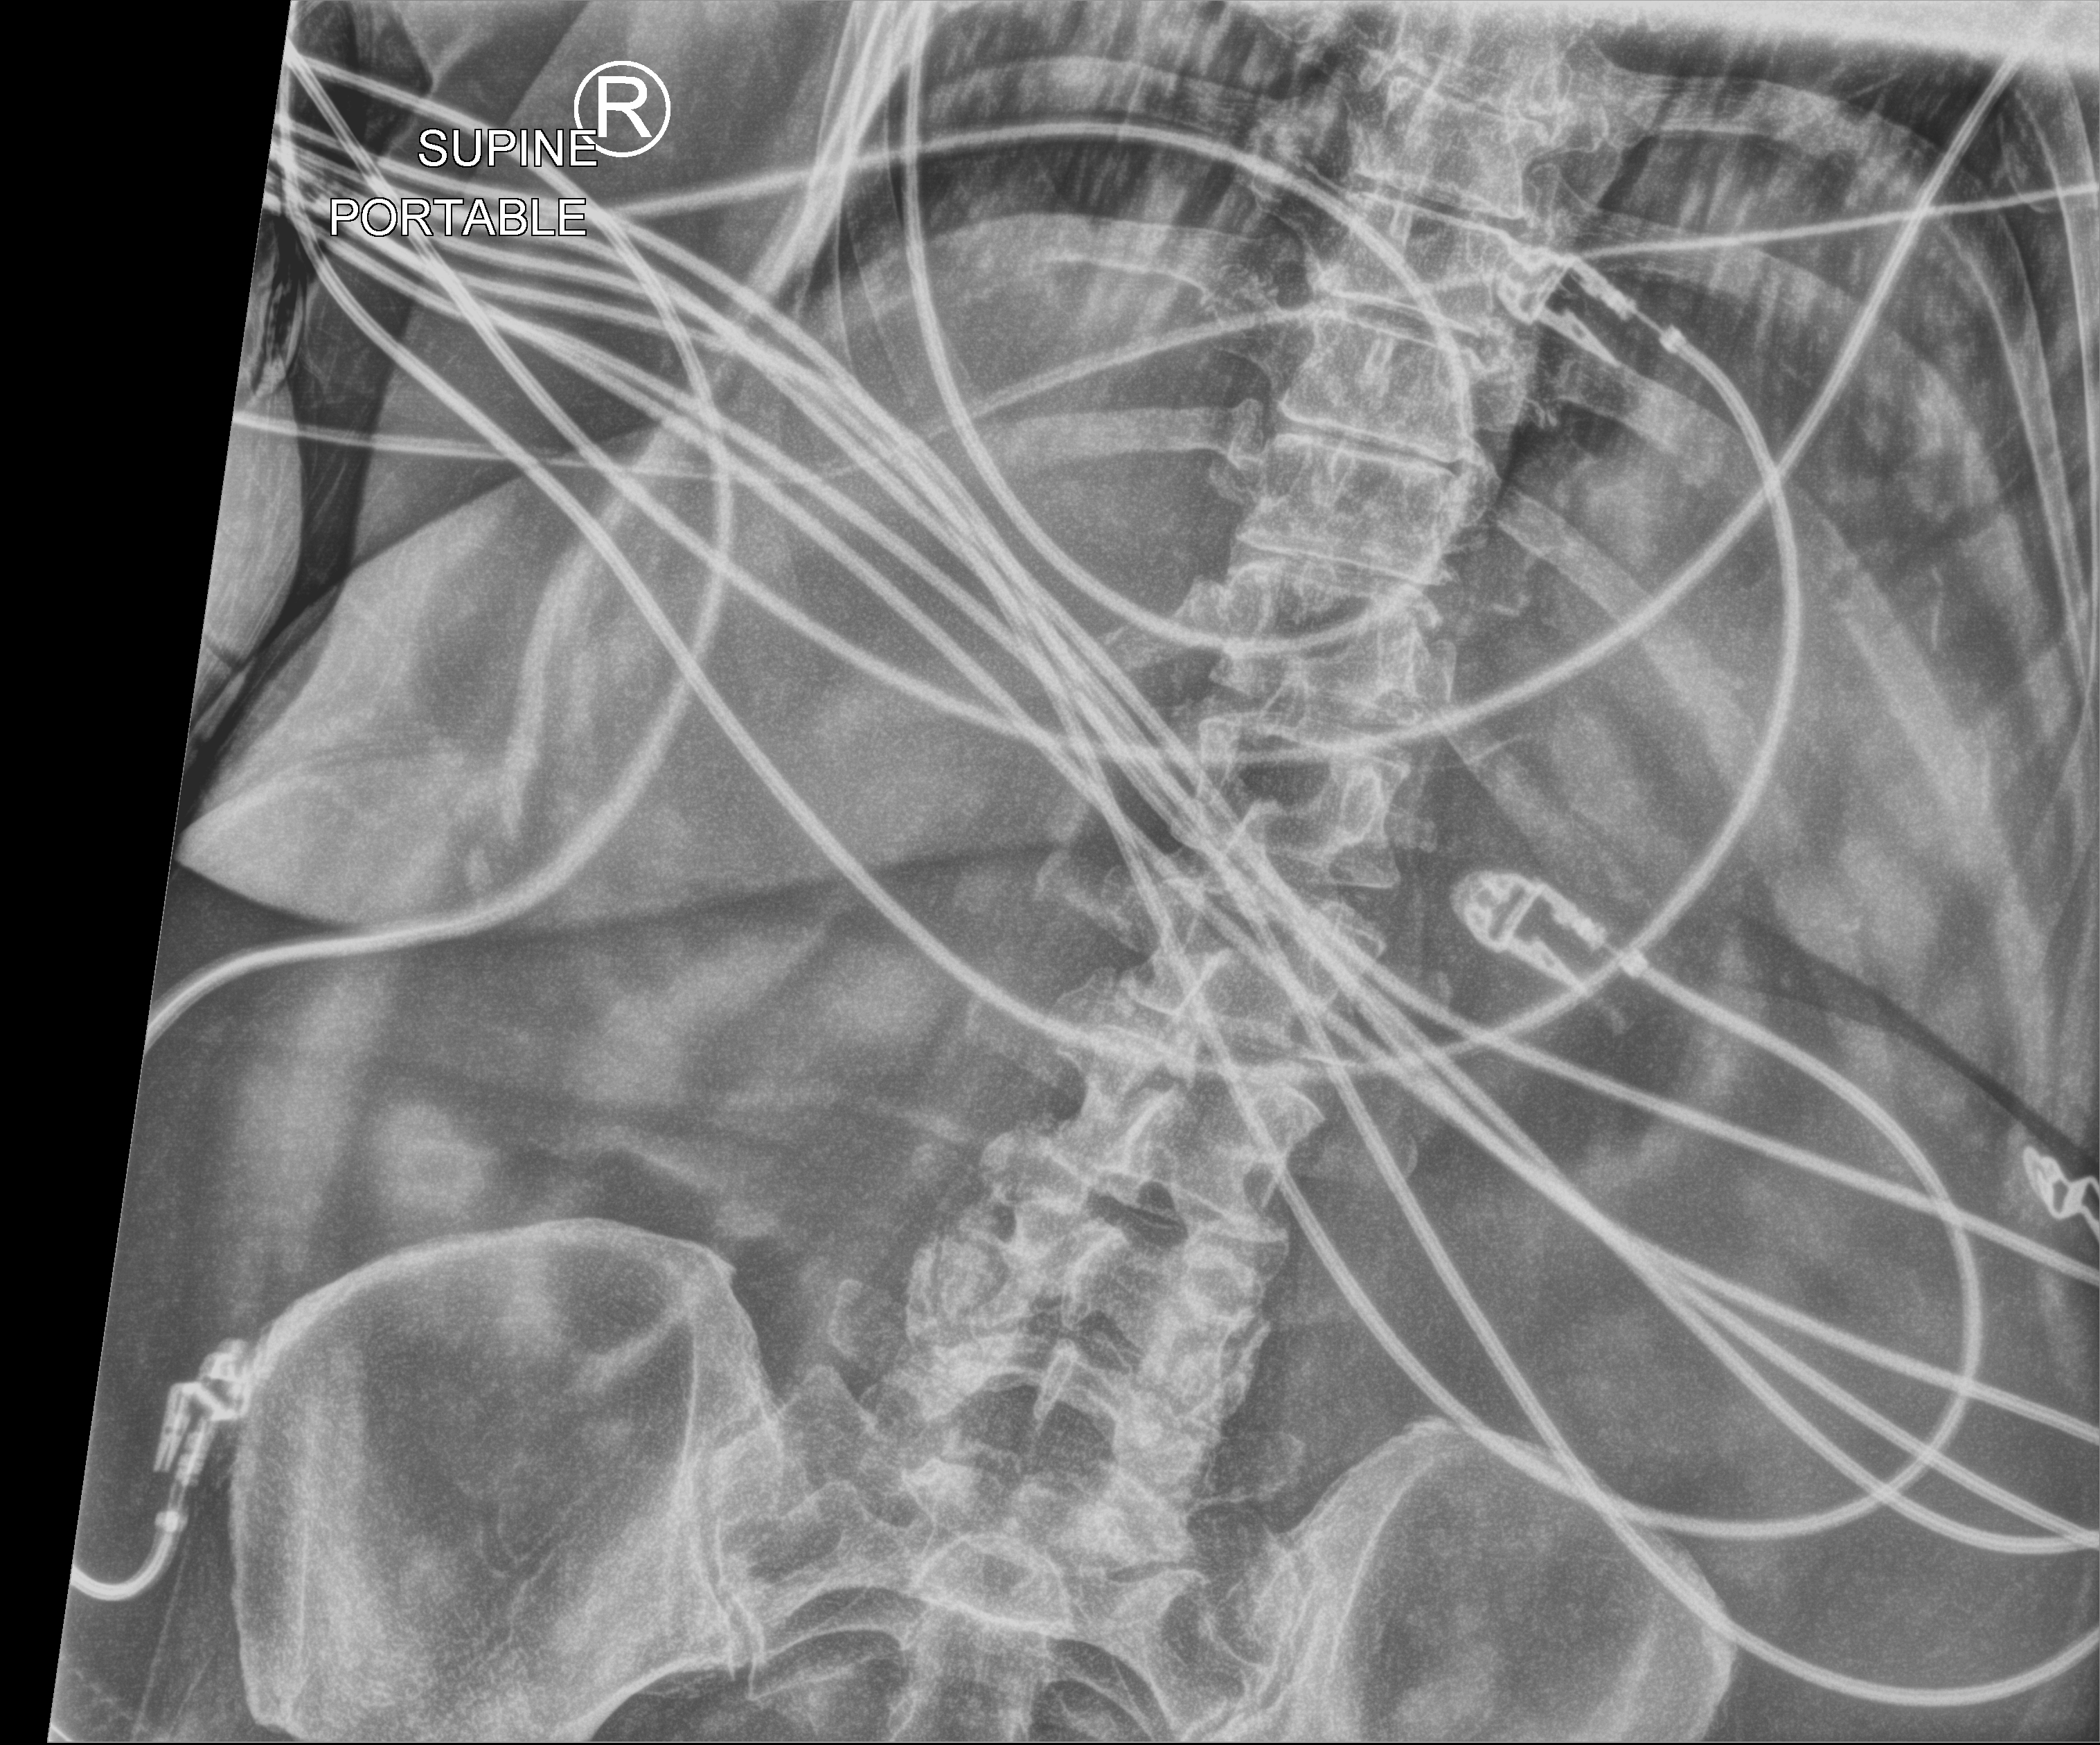
Abdomen X-ray (portable). Patient hospitalised with COVID-19; female, aged 60–74 years.
Hospital-stay facts (about this admission, not read from this image; timing relative to this image not recorded): admitted to intensive care during this hospital stay: yes; COPD (admission record): no; diabetes (admission record): no.